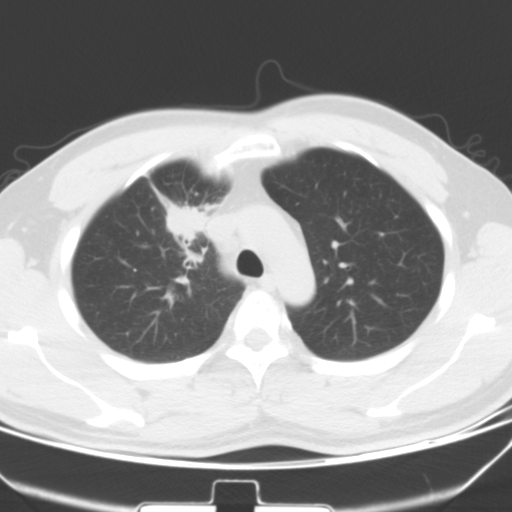
Chest CT, one axial slice. Slice 44 of 60 in the series (ordered by position). 120 kVp. Lung window (W 1500 / L -600 HU). 5 mm slice thickness. 512 × 512 image matrix. Male patient, age 35 years. Case-level facts recorded for this patient, not image findings: clinical TNM (as recorded): T1c N1 M1b.
Outlined on this slice (bounding box drawn by a radiologist):
- lung tumour (recorded histology: adenocarcinoma): bounding box <165,200,207,239> (left, top, right, bottom; pixels)